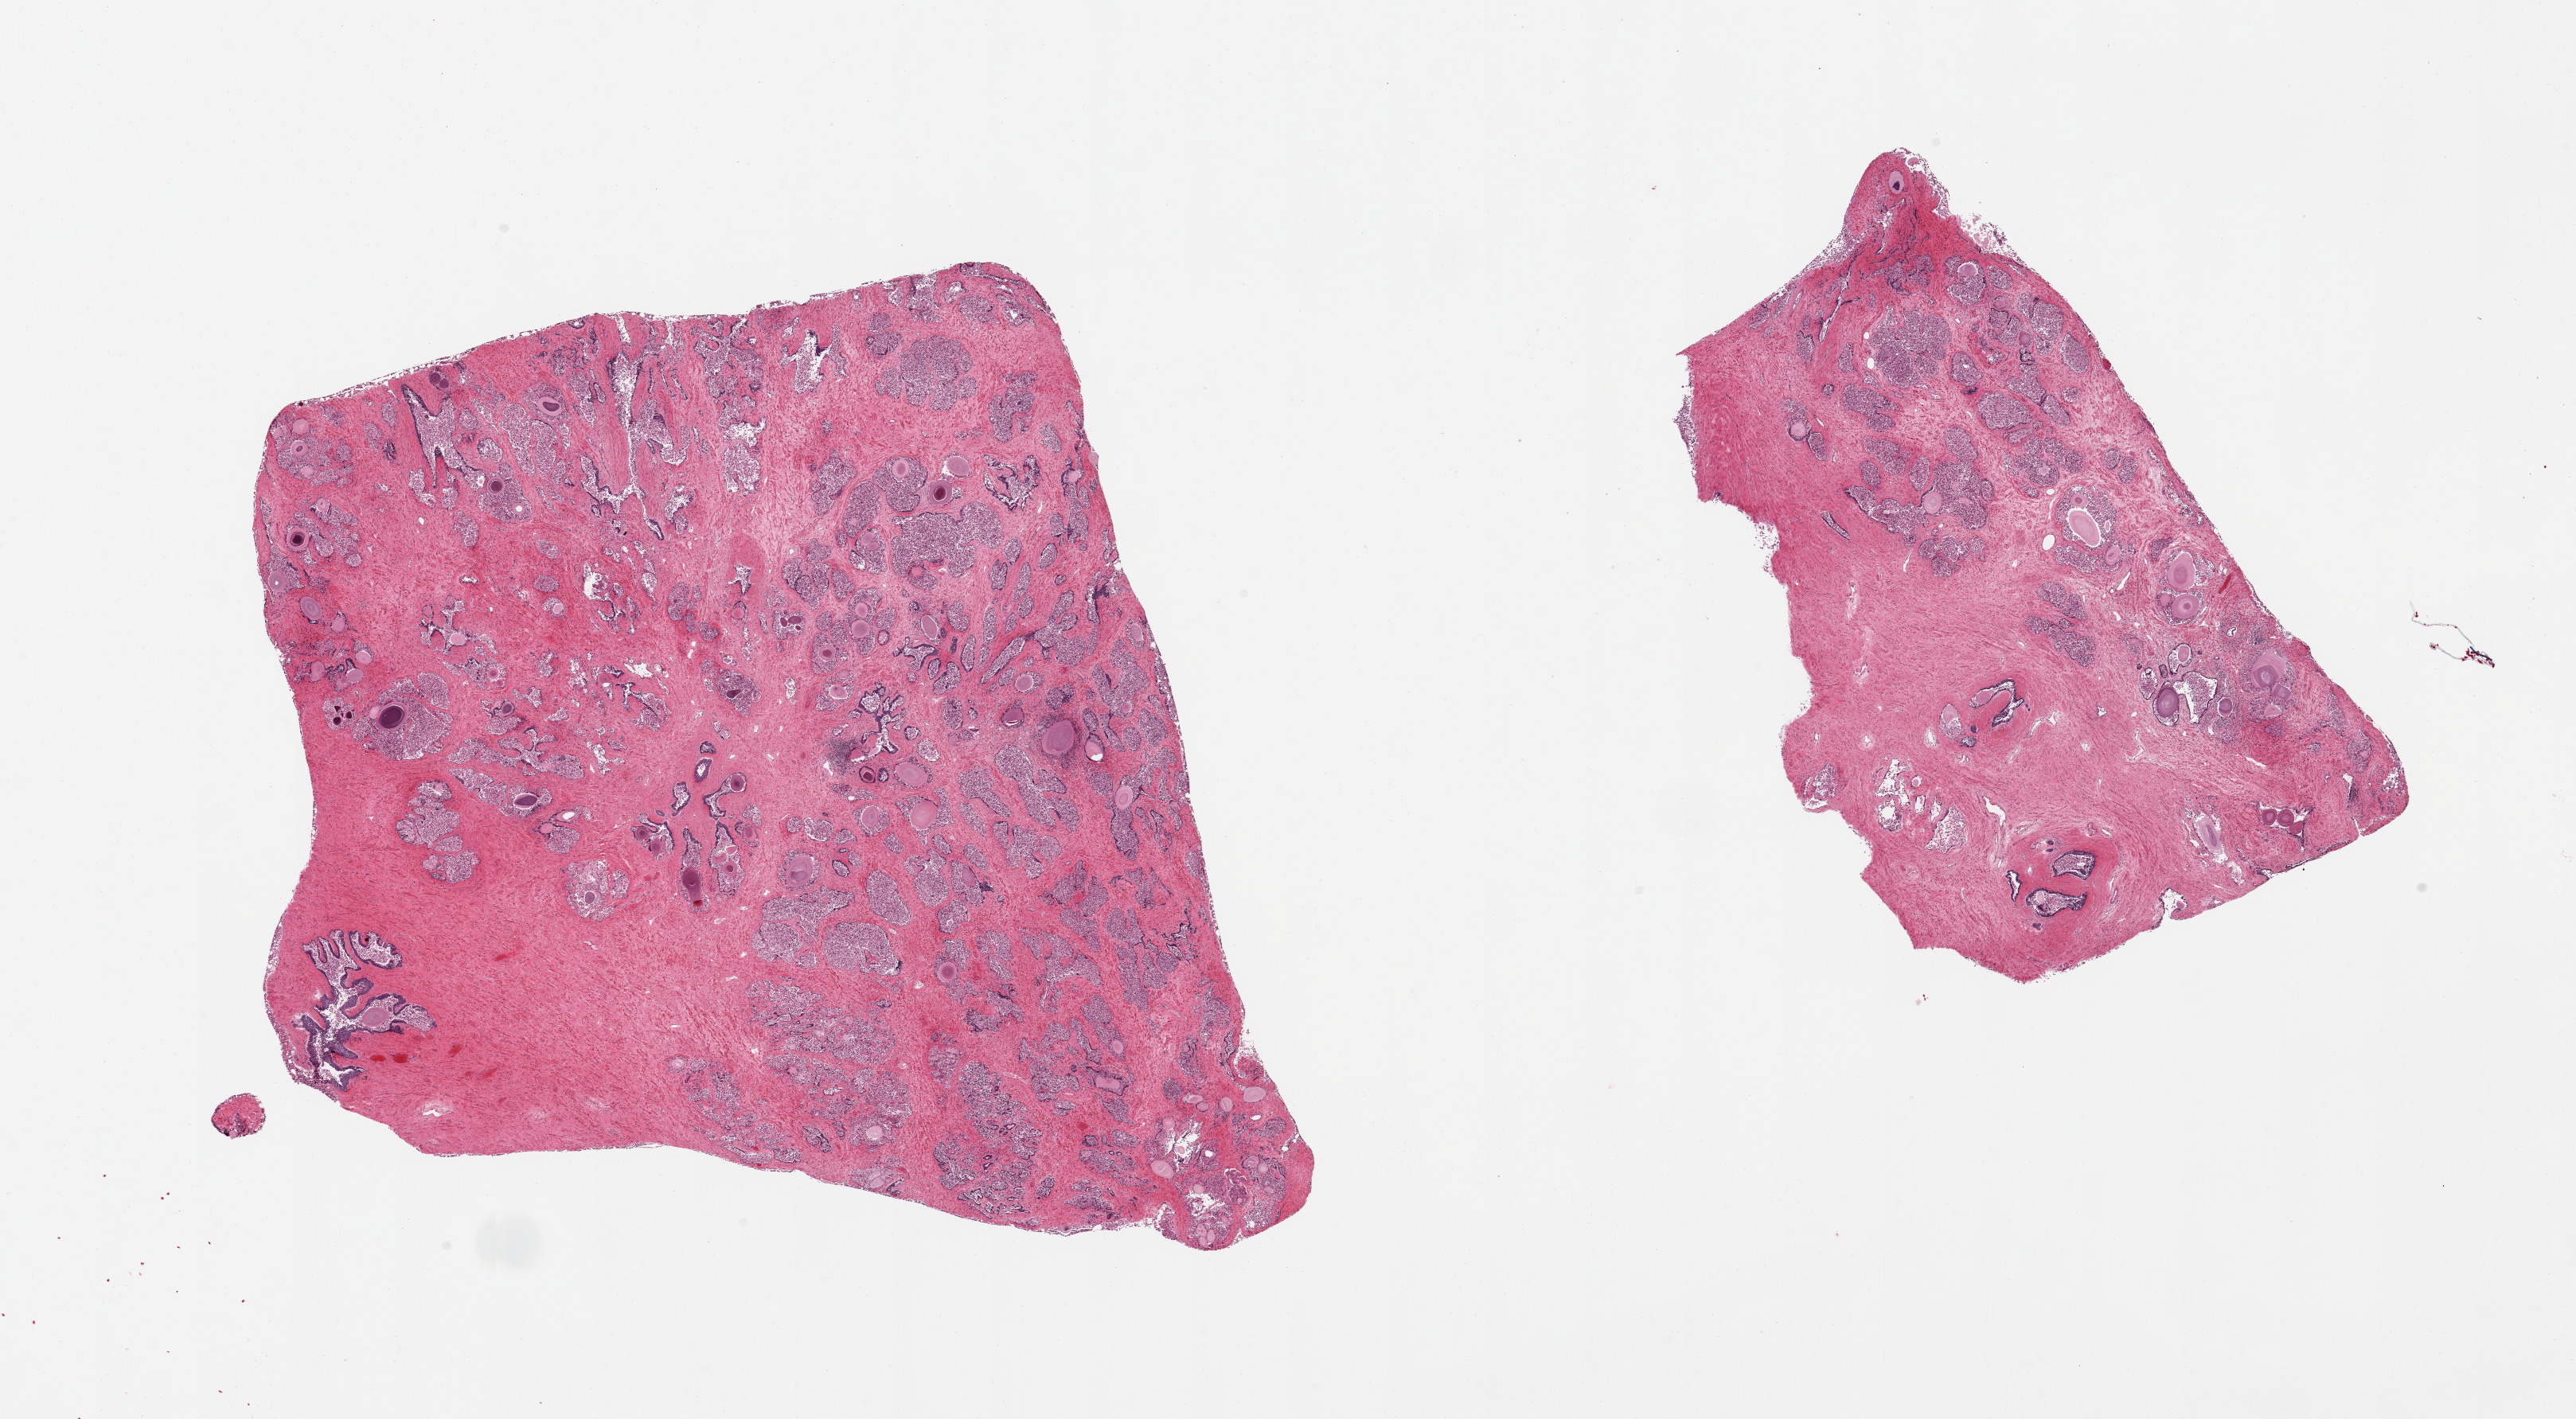
H&E whole-slide image — low-resolution overview of the scanned area, about 25.6 x 14.1 mm, PAXgene-fixed, paraffin-embedded tissue, section of prostate (target tissue), tissue donor sample. Male donor.
• reviewer comment on this tissue sample: 2 pieces; fibromuscular stroma and partially autolyzed glandular component with numerous corpora amylacea, focal chronic prostatitis